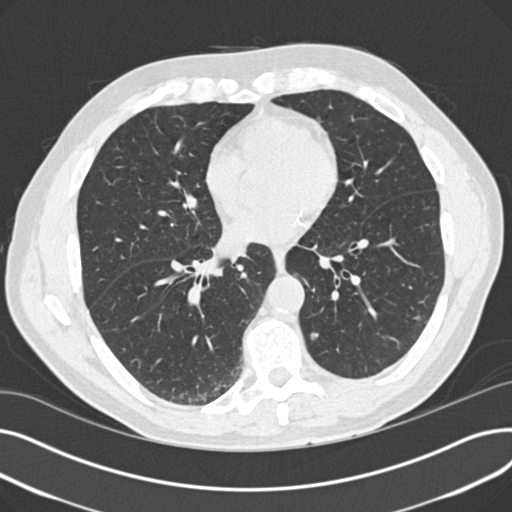
Axial slice from a low-dose chest CT screening exam, second screening round (one year after baseline), lung window (W 1500 / L -600 HU), 2 mm slice thickness, slice 97 of 163 in the series, 512 × 512 image matrix. Male, age 64 years at enrolment. Former smoker at enrolment.
Lesion marked by an expert reader, bounding box (x1, y1, x2, y2) in pixels: (298, 318, 336, 355). Screening reader's record for this exam (one nodule recorded; not confirmed to be the boxed lesion): non-calcified nodule or mass ≥4 mm, left lower lobe, 6 × 5 mm, smooth margins, ground glass attenuation, pre-existing on the prior screen: yes; interval growth: no. Participant outcome: lung cancer diagnosed 417 days after this screen — adenocarcinoma with mixed subtypes, left lower lobe, well differentiated (G1), stage IA (AJCC 6th edition), 7 mm at pathology.